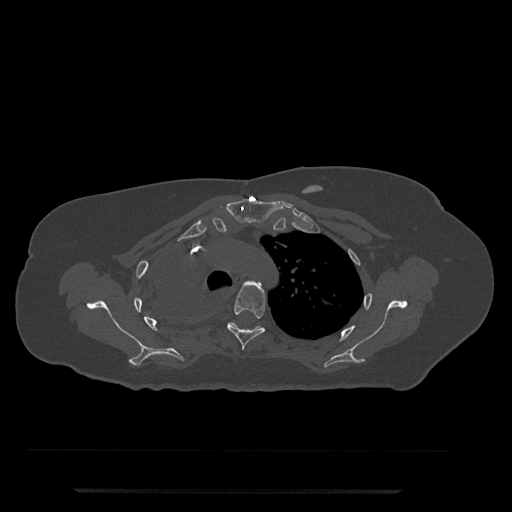
CT including the spine, one axial slice. Slice 586 of 797 in the series (ordered by position). Reconstruction kernel Br40s/3. Bone window (W 1800 / L 400 HU). 0.5 mm slice thickness. 512 × 512 image matrix, field of view 440 × 440 mm. Female patient, age 51 years. Case-level facts recorded for this patient, not image findings: primary cancer: neuro.
Annotated regions visible in this slice (semi-automatic segmentation, software-assisted and operator-edited):
- T3 vertebra: bounding box [x1, y1, x2, y2] px = [245, 281, 262, 287]
- T4 vertebra: [227, 282, 266, 350]
- T5 vertebra: [229, 322, 263, 331]